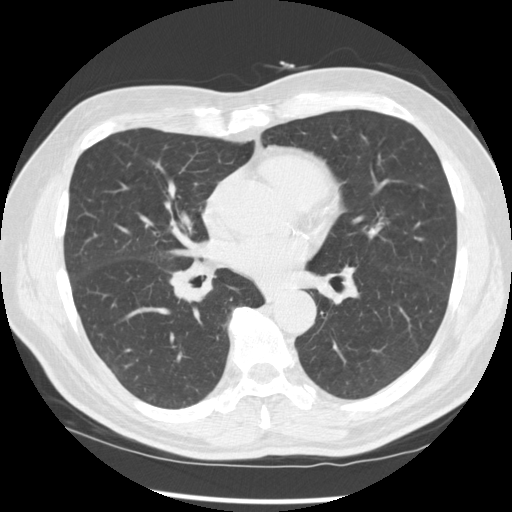
Low-dose screening chest CT, one axial slice; slice 139 of 277 in the series (ordered by position); 120 kVp; lung window (W 1500 / L -600 HU); 512 × 512 image matrix, field of view 365 × 365 mm.
Outlined on this slice (manually delineated by an expert):
- lesion 1 (tumor, middle lobe of right lung): box from (x=169, y=271) to (x=205, y=303) px